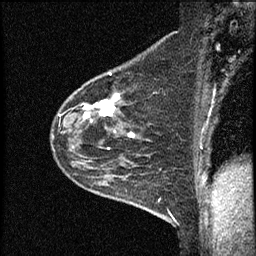
Breast MRI (dynamic contrast-enhanced), one sagittal slice. Slice 45 of 60 in the series (ordered by position). Dynamic contrast-enhanced study with each time point stored as its own series, time point 2 of 4 at this slice position (early post-contrast, ordered by acquisition time). 1.5 T. TE 4.2 ms, TR 17.6 ms. 2 mm slice thickness. 256 × 256 image matrix, field of view 200 × 200 mm. Patient: female, 53 years. Case-level facts recorded for this patient, not image findings: setting: breast cancer imaged before/during neoadjuvant chemotherapy; receptor status: HR-positive, HER2-negative.
Annotated regions visible in this slice (semi-automatically segmented with operator editing):
- analysis volume of interest (the breast-tissue region the enhancement analysis was run in; not a lesion): bounding box [x1, y1, x2, y2] px = [50, 69, 153, 199]
- tumour enhancement mask (voxels above the 100 % enhancement threshold inside the analysis volume of interest): [83, 94, 134, 137]